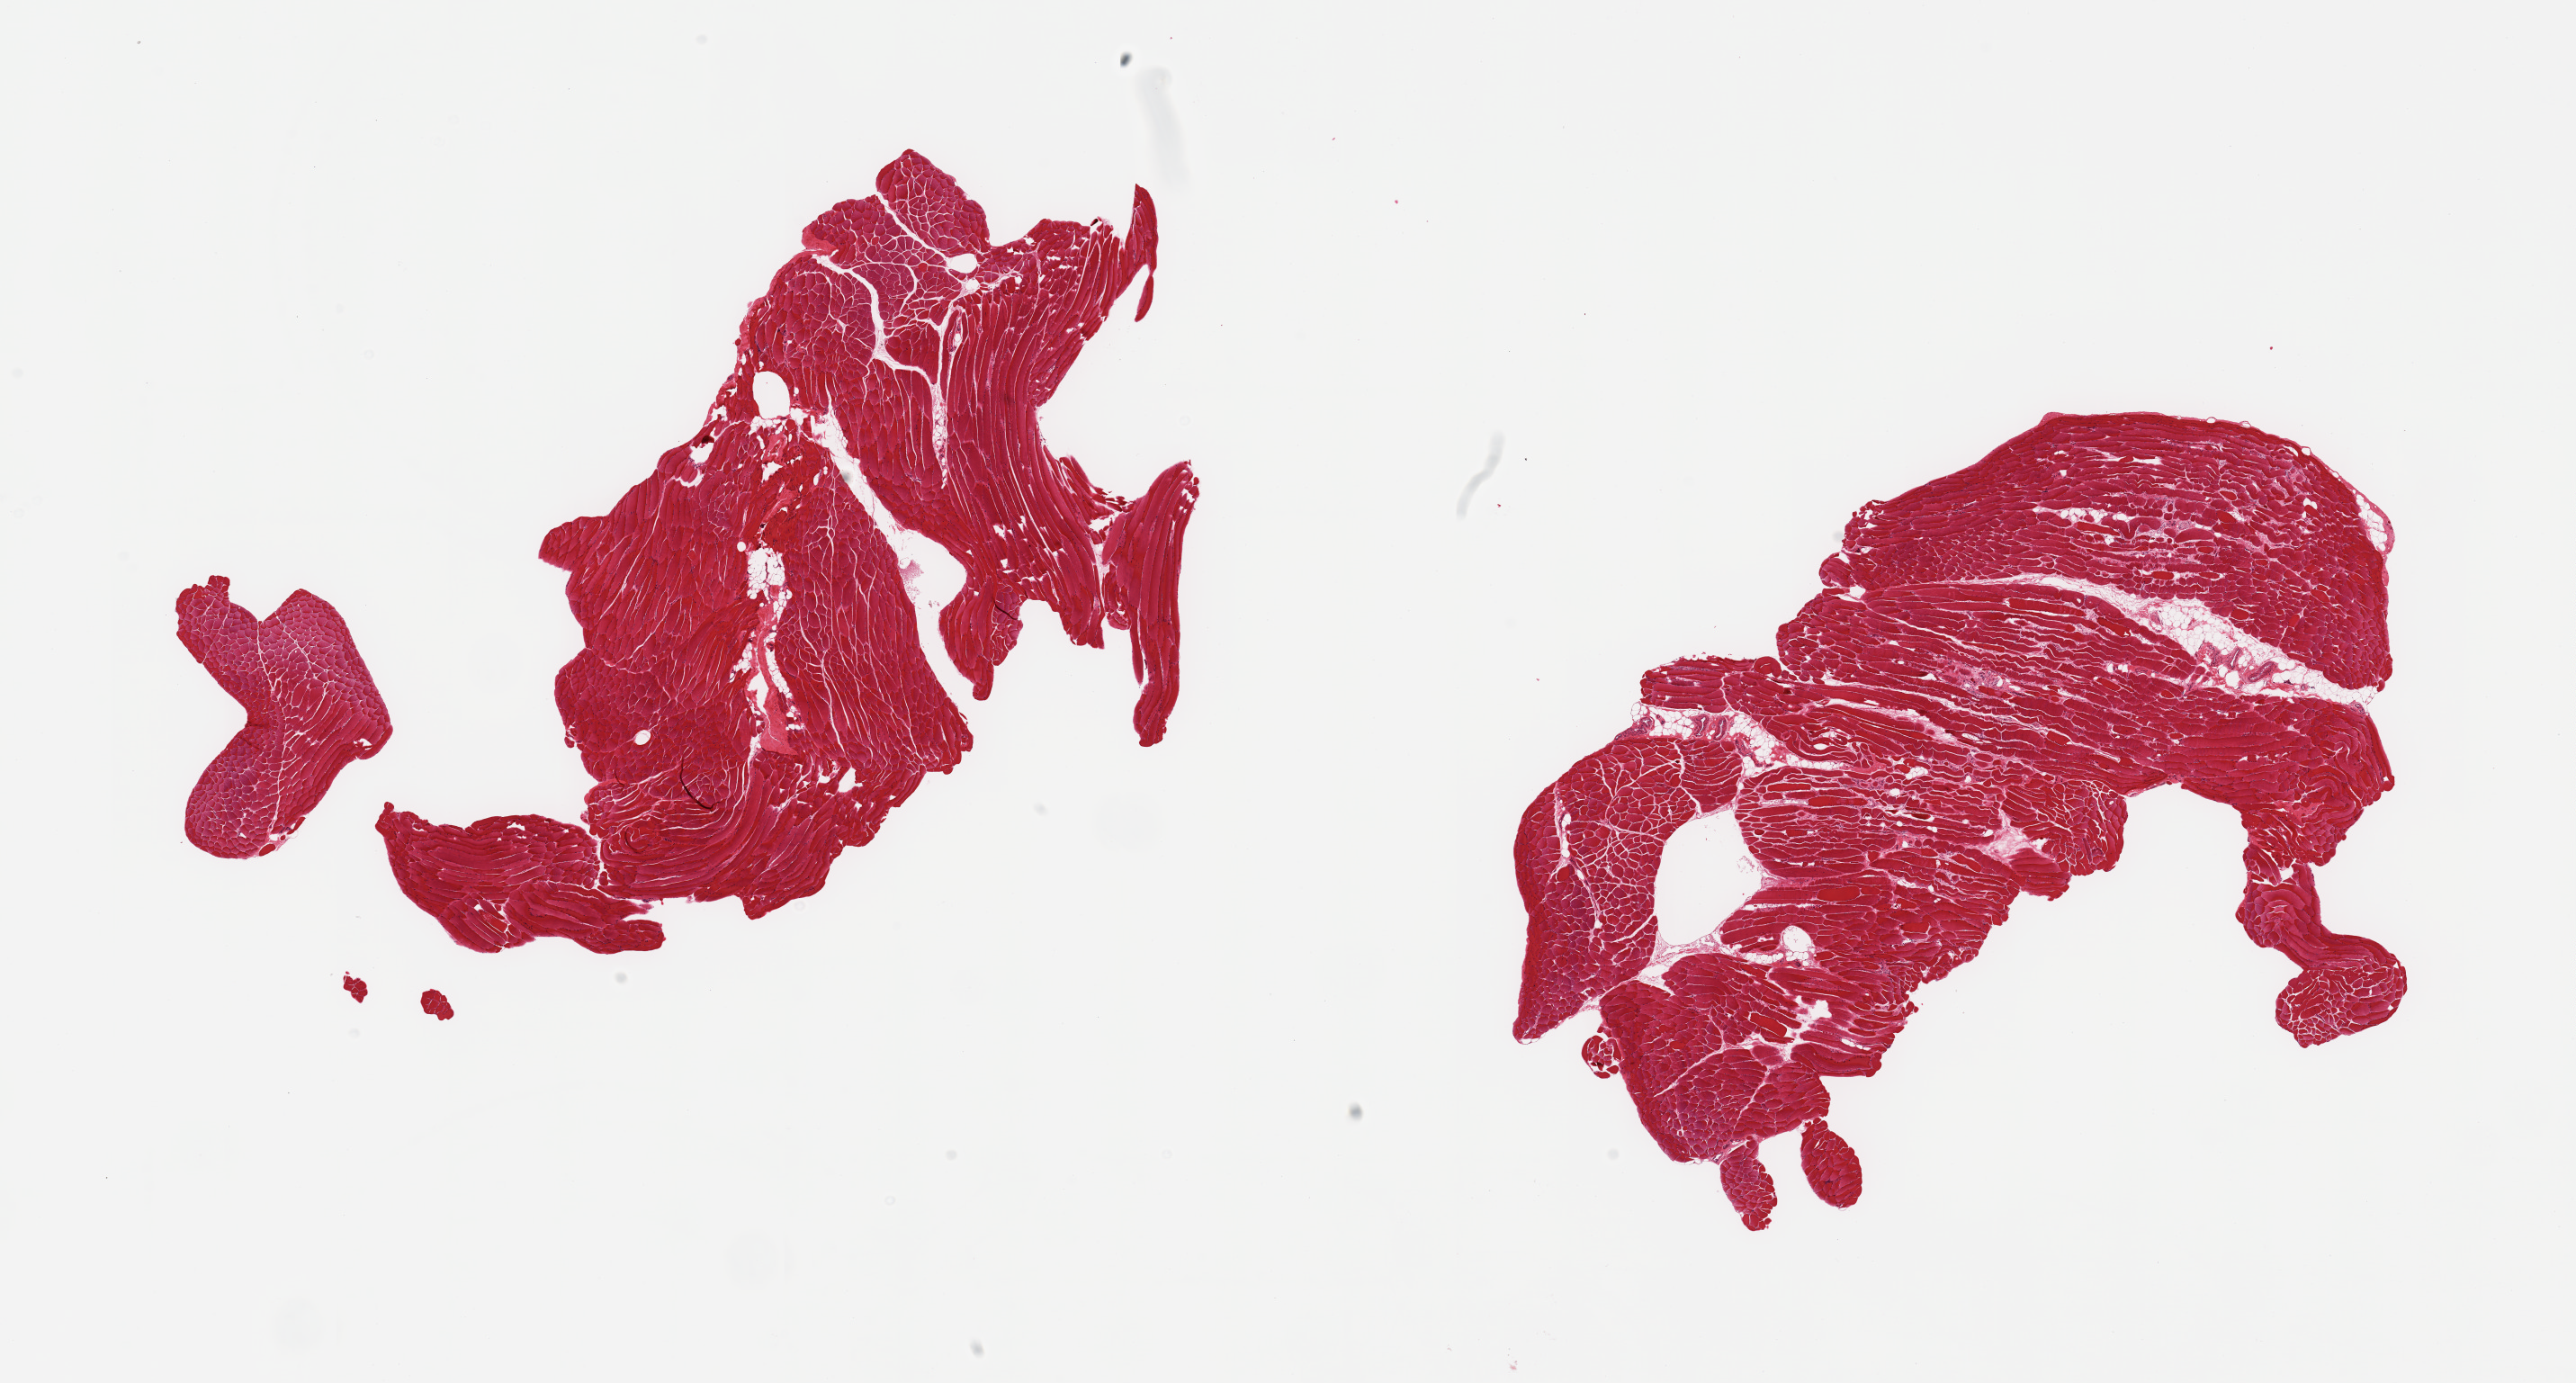
Whole-slide image, H&E stain, whole scanned area (about 22.6 x 12.2 mm) shown as a low-resolution overview, PAXgene-fixed paraffin-embedded (PFPE) section, target tissue: skeletal muscle, donor tissue sample. Donor: male.
Pathologist's review note for this sample: 2 pieces, interstitial fat/vascular elements are ~10% of tissue.